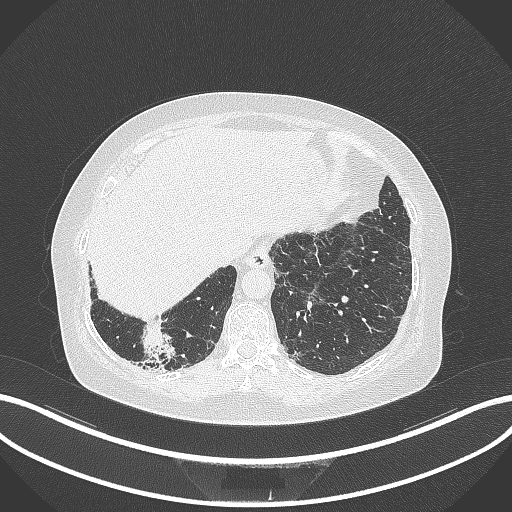
Chest CT, one axial slice; position 25 of 296 along the scan axis; lung window (W 1500 / L -600 HU); 1 mm slice thickness; 512 × 512 image matrix, field of view 400 × 400 mm. Female patient, age 65 years. Case-level facts recorded for this patient, not image findings: clinical TNM (as recorded): T2b N1 M0; histopathological grade: G1.
Structures marked on this image (rectangle marked by the reading radiologist):
- lung tumour (recorded histology: adenocarcinoma): bounding box (x1, y1, x2, y2) in pixels: (135, 324, 179, 364)